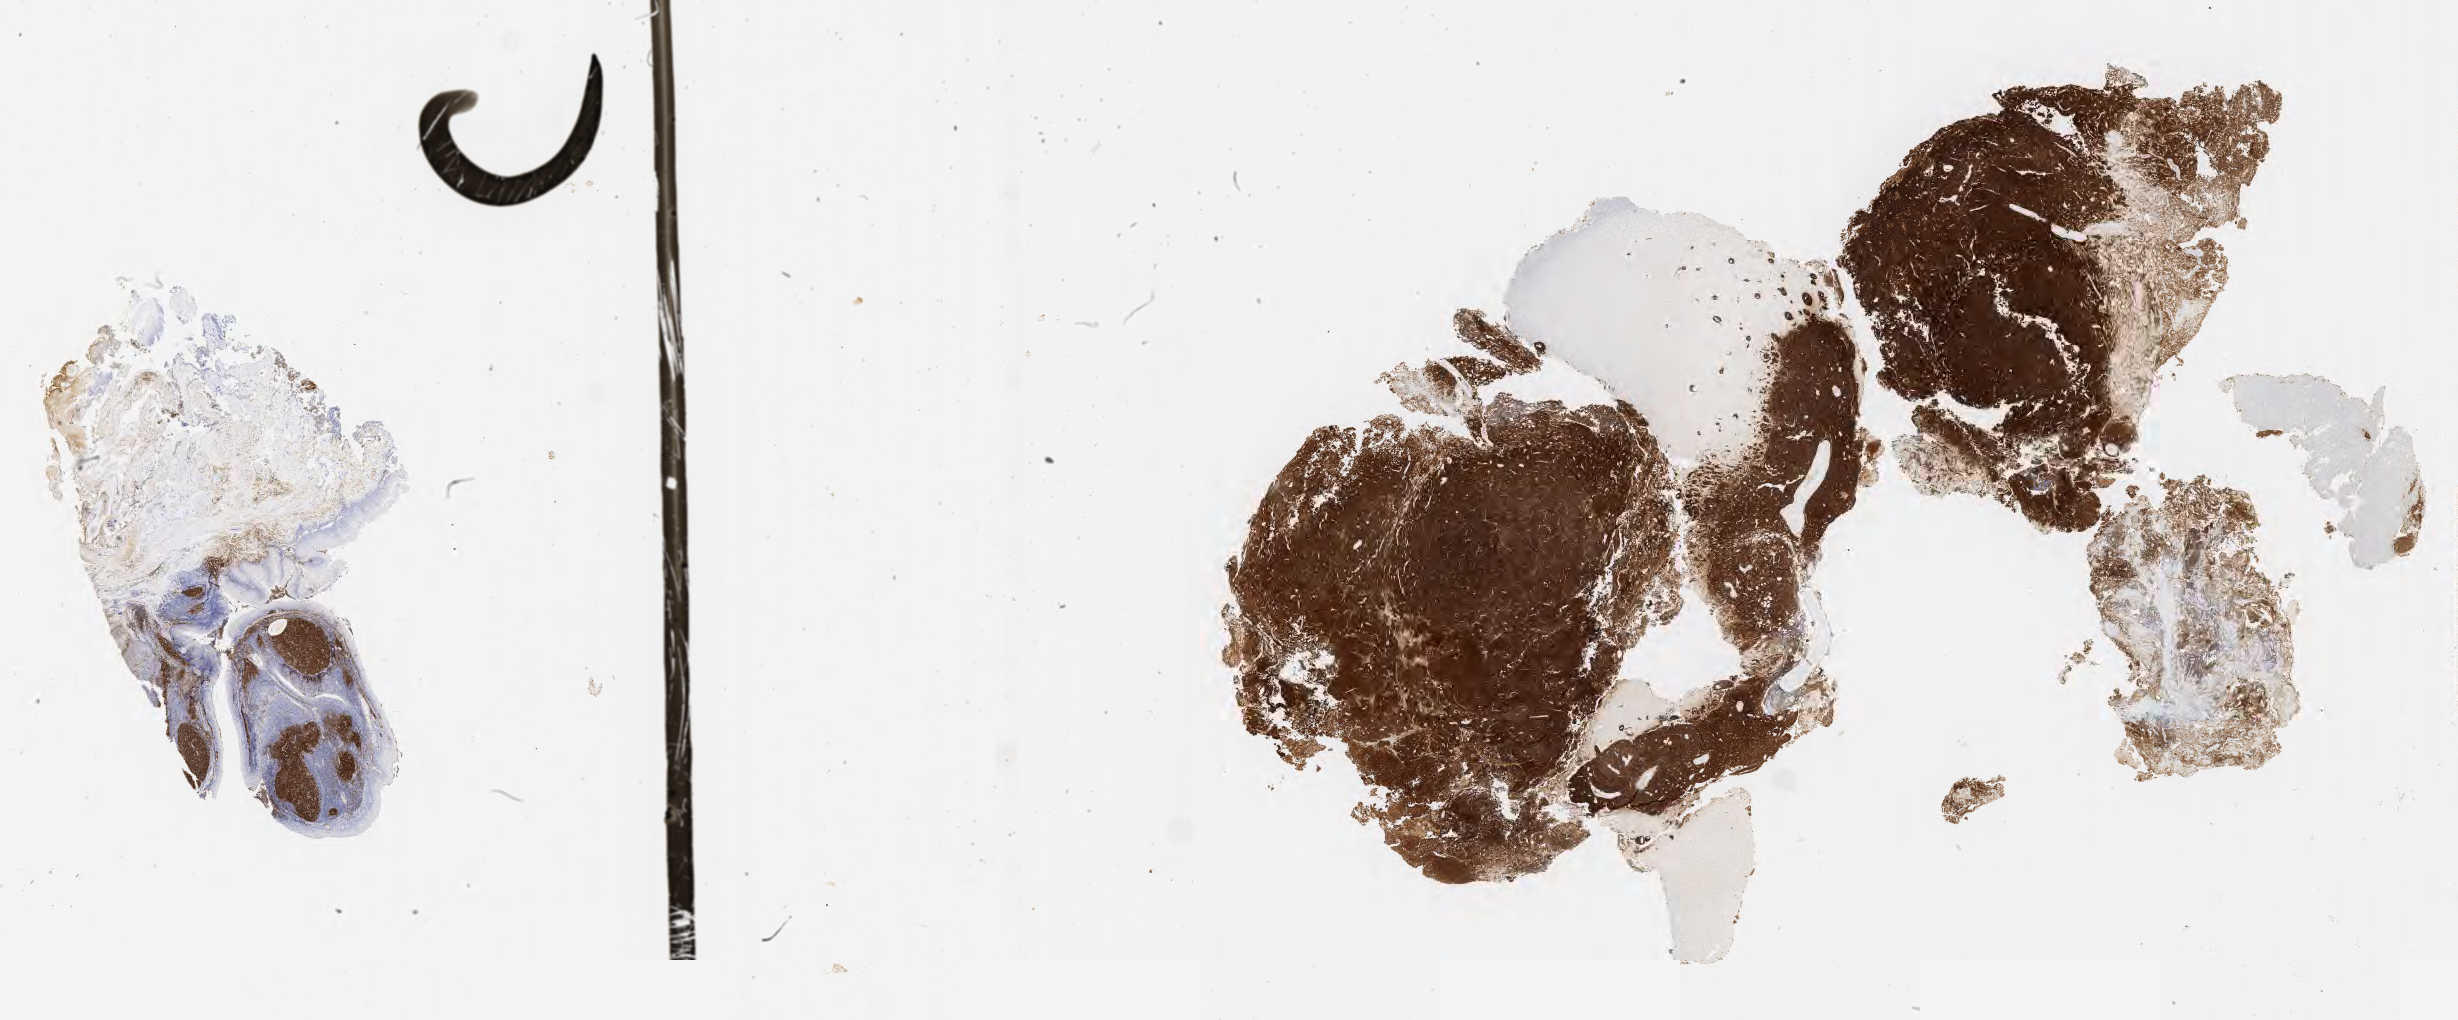
IHC for CD10, whole-slide image, shown as a low-resolution overview of the whole scanned area (about 39.8 x 16.5 mm), specimen: tumor tissue. Female patient, aged 73.
Histologic diagnosis: Burkitt lymphoma, NOS.